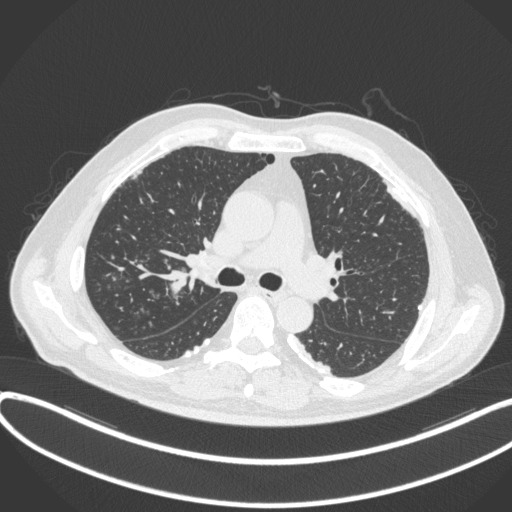
Chest CT, one axial slice; position 262 of 455 along the scan axis; 120 kVp; lung window (W 1500 / L -600 HU); 1 mm slice thickness; 512 × 512 image matrix, field of view 400 × 400 mm. Male patient, age 58 years. Case-level facts recorded for this patient, not image findings: clinical TNM (as recorded): T1c N0 M0.
Outlined on this slice (rectangle marked by the reading radiologist):
- lung tumour (recorded histology: squamous cell carcinoma): bounding box (x1, y1, x2, y2) in pixels: (162, 262, 194, 296)